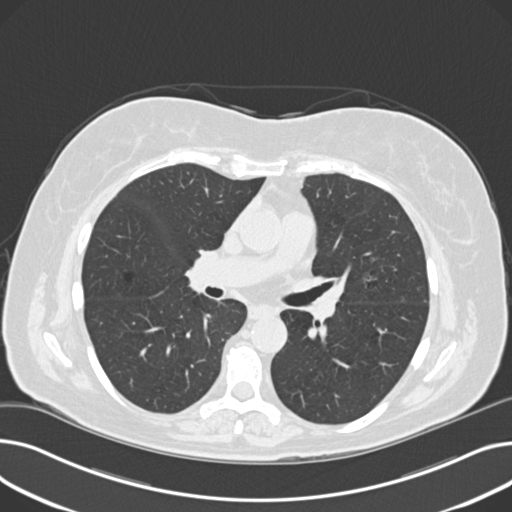
Chest CT (low-dose screening protocol), one axial image. Third screening round (two years after baseline). Lung window (W 1500 / L -600 HU). Standard (soft-tissue) reconstruction kernel (B30f). 120 kVp. Slice 96 of 203 in the series. Female participant, aged 60 years at enrolment. Current smoker at enrolment.
Expert reader's lesion annotation, bounding box [x1, y1, x2, y2] px = [354, 267, 392, 299]. The screening reader recorded 8 non-calcified nodules or masses ≥4 mm on this exam (right upper lobe, lingula, lingula, right middle lobe, right lower lobe, left lower lobe, left lower lobe, left lower lobe); which of them this box marks is not recorded. Official screen result: positive, other.